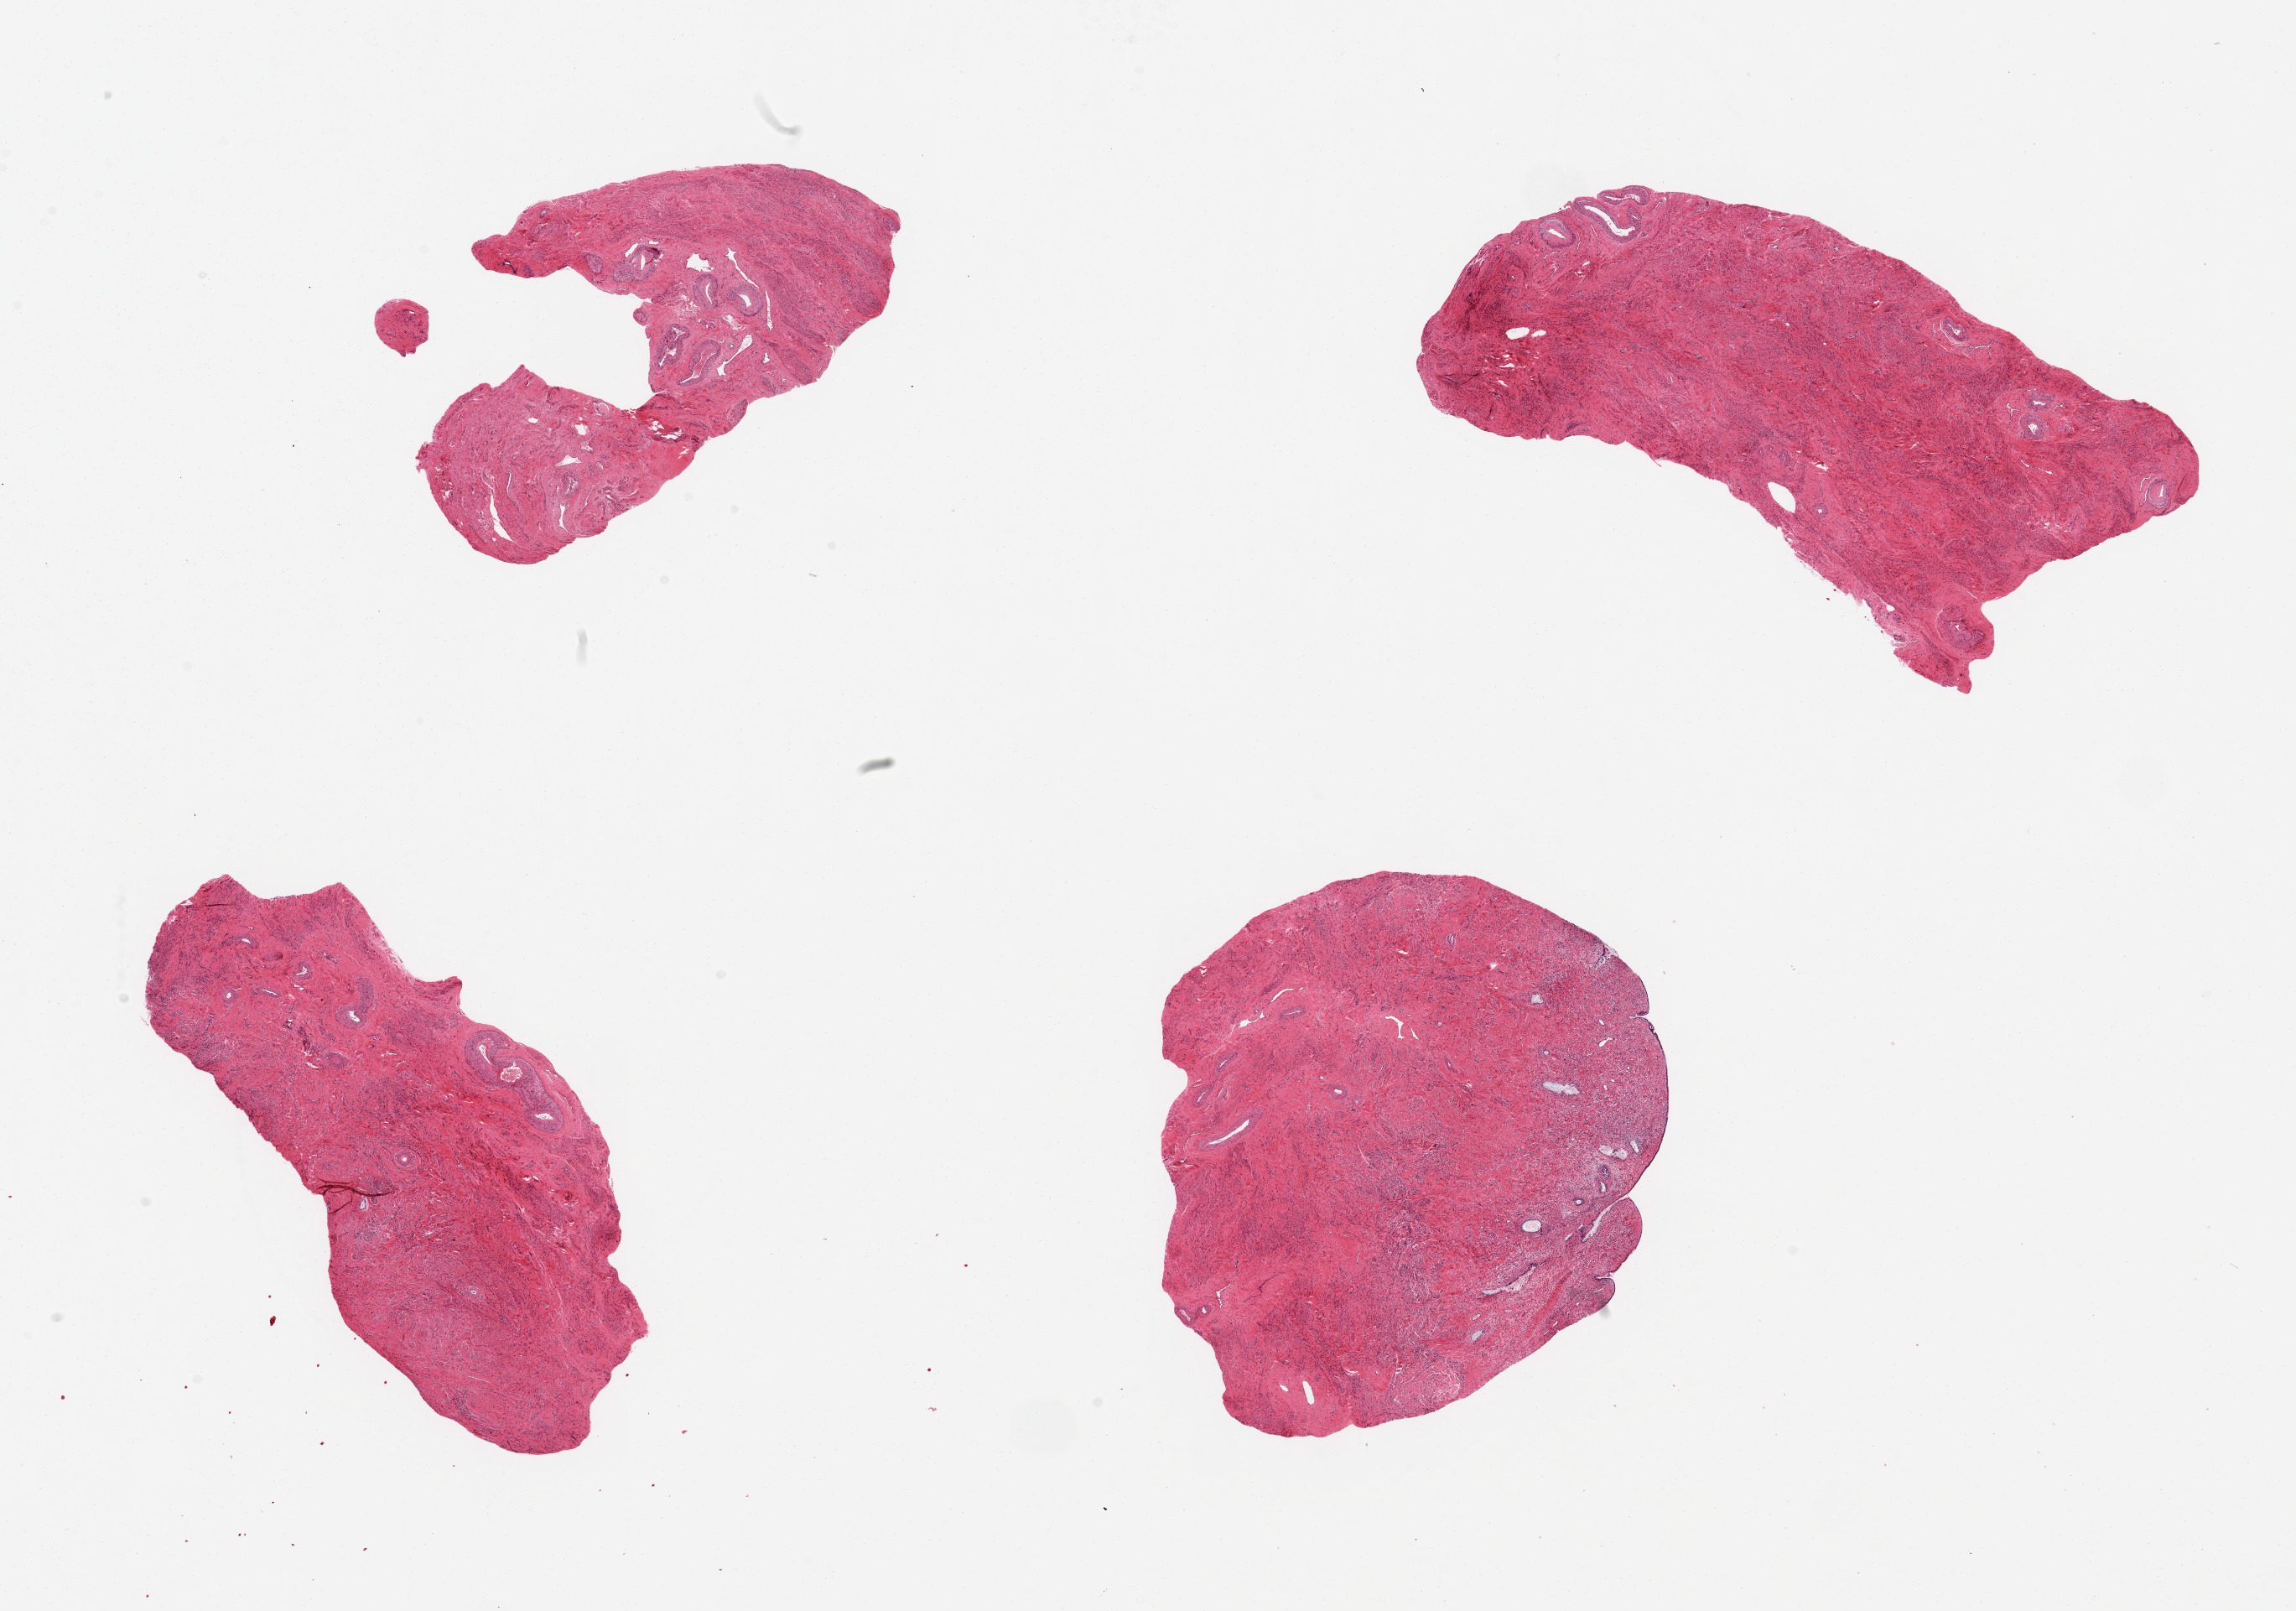
Digitized hematoxylin and eosin (H&E)-stained section, brightfield, a low-resolution overview of the entire scanned area, about 21.7 x 15.2 mm. PAXgene-fixed, paraffin-embedded tissue. Target tissue: endocervix. Tissue donor sample. Donor: female.
Review note (as recorded): 4 pieces up to 6x3 mm; one piece has columnar surface and glands; others have no epithelium.